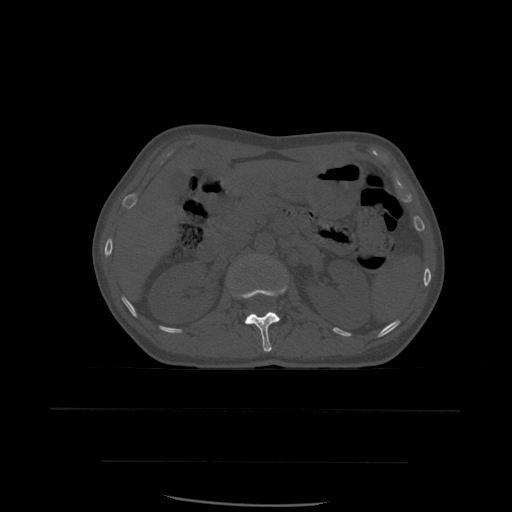
CT including the spine, one axial slice. Slice 243 of 574 in the series (ordered by position). Bone window (W 1800 / L 400 HU). 1.25 mm slice thickness. 512 × 512 image matrix, field of view 392 × 392 mm. Patient age 48 years. Case-level facts recorded for this patient, not image findings: primary cancer: lung.
Outlined on this slice (semi-automatic segmentation, software-assisted and operator-edited):
- L1 vertebra: bounding box <230,283,288,352> (left, top, right, bottom; pixels)